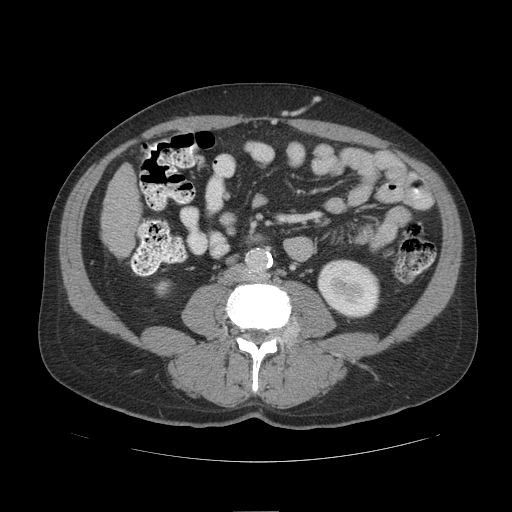
Contrast-enhanced abdominal CT (liver protocol), one axial slice; position 25 of 109 along the scan axis; reconstruction kernel STANDARD; 140 kVp; soft-tissue window (W 400 / L 40 HU); 2.5 mm slice thickness; 512 × 512 image matrix, field of view 420 × 420 mm. Case-level facts recorded for this patient, not image findings: diagnosis: hepatocellular carcinoma (patient treated with transarterial chemoembolisation; whether this scan precedes or follows treatment is not stated here); TNM stage (as recorded): Stage-IIIB; Child-Pugh class: A; tumour nodularity: multinodular.
Structures marked on this image (semi-automatic segmentation, software-assisted and operator-edited):
- liver parenchyma outside the tumour (the mass and vessels are separate outlines, so this box may not span the whole liver): bounding box <102,164,140,256> (left, top, right, bottom; pixels)